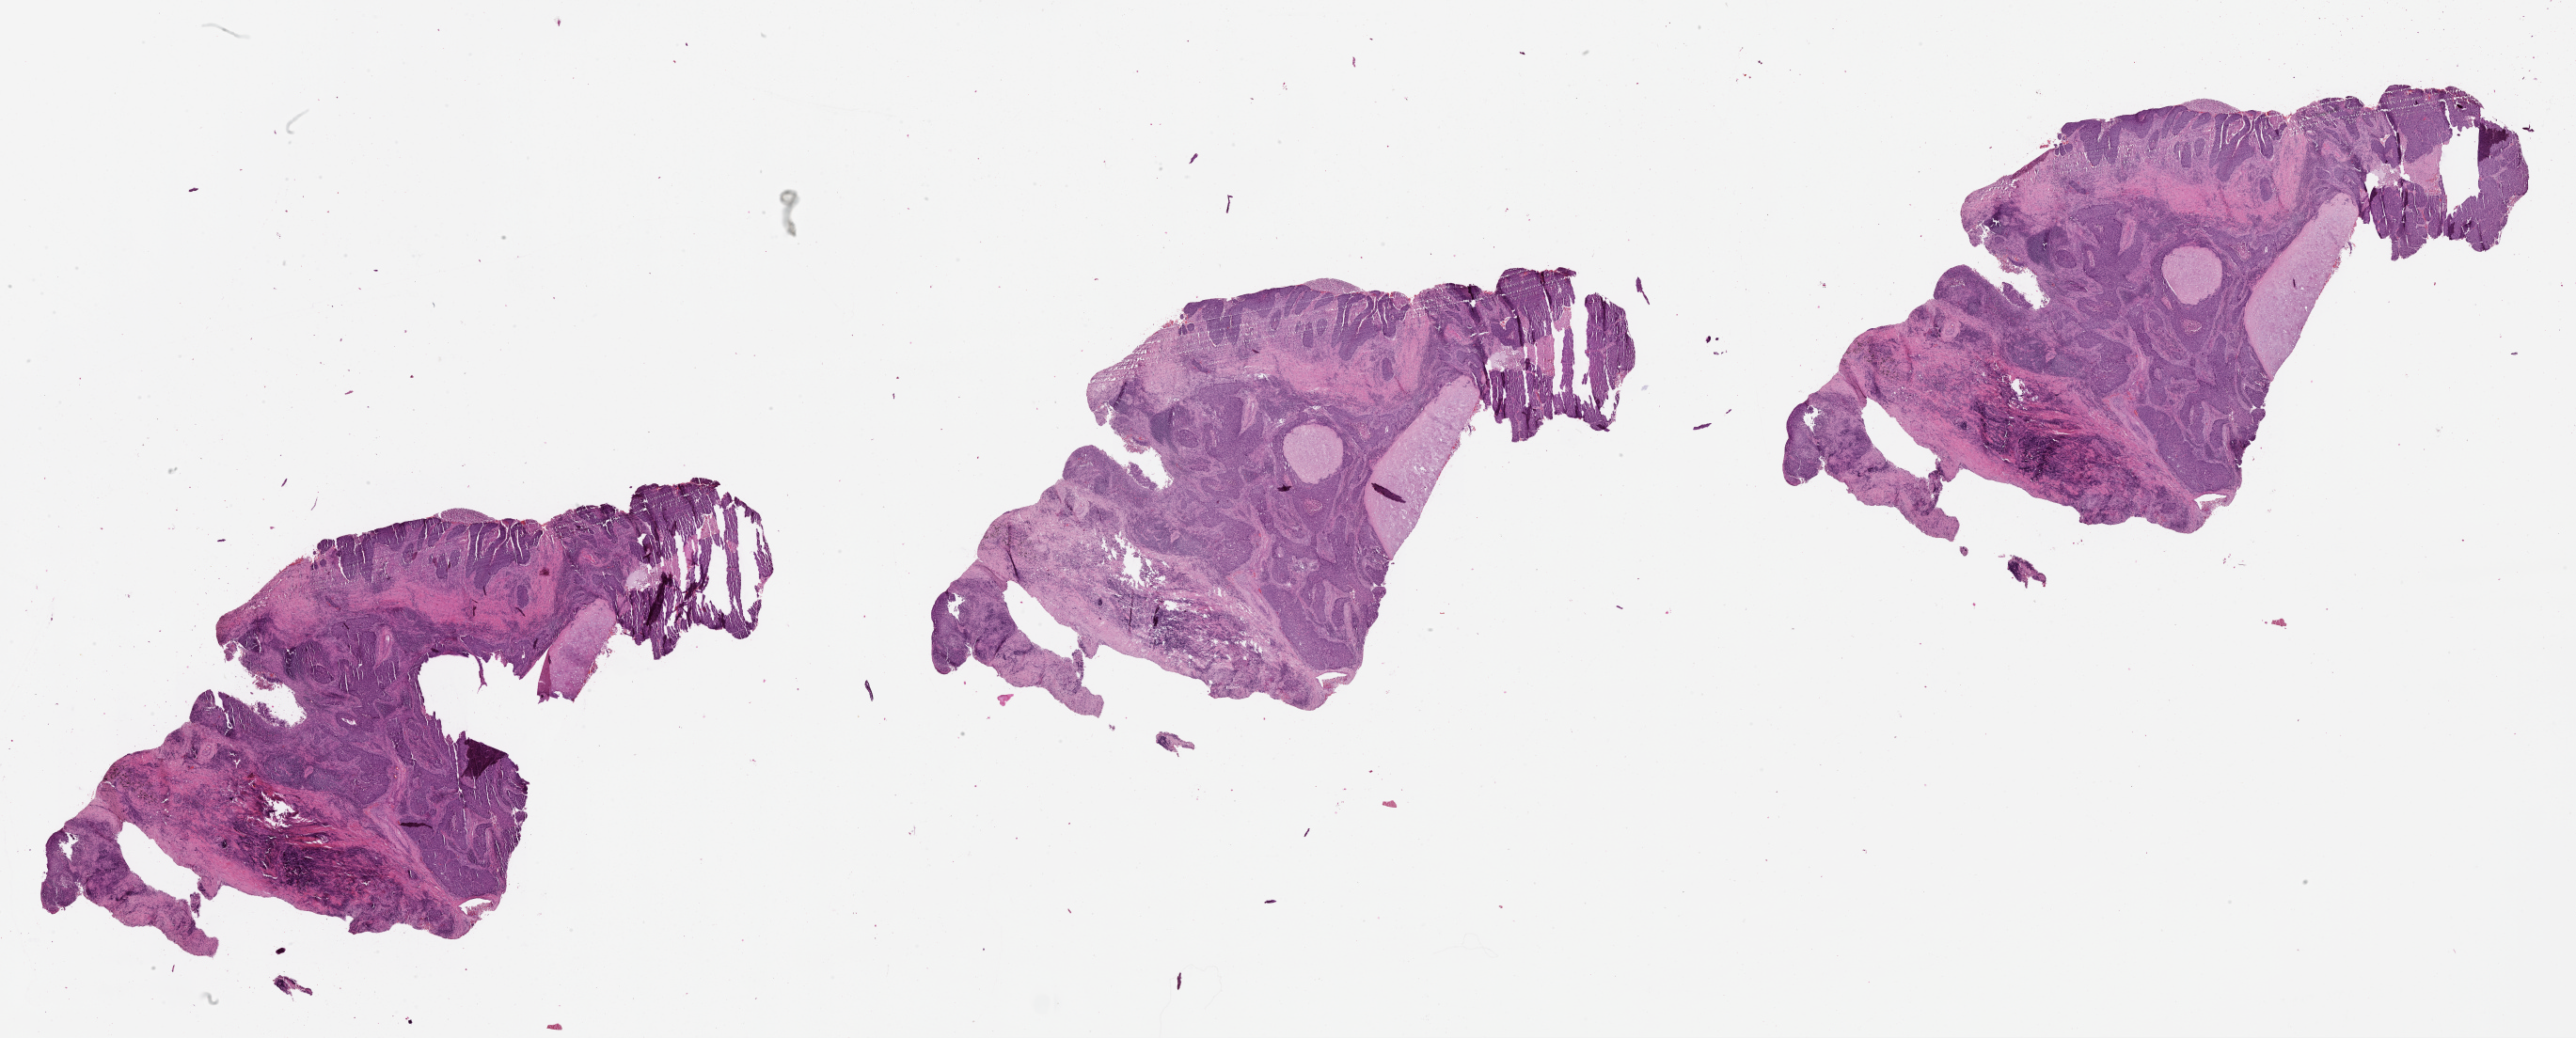
Digitized H&E tissue section (whole slide), shown as a low-resolution overview of the whole scanned area (about 44.1 x 17.8 mm, acquisition: 20x scan); lung, tumour tissue. Patient: male, age 58 years.
Patient diagnosis (cohort enrolment): squamous cell carcinoma (lung).